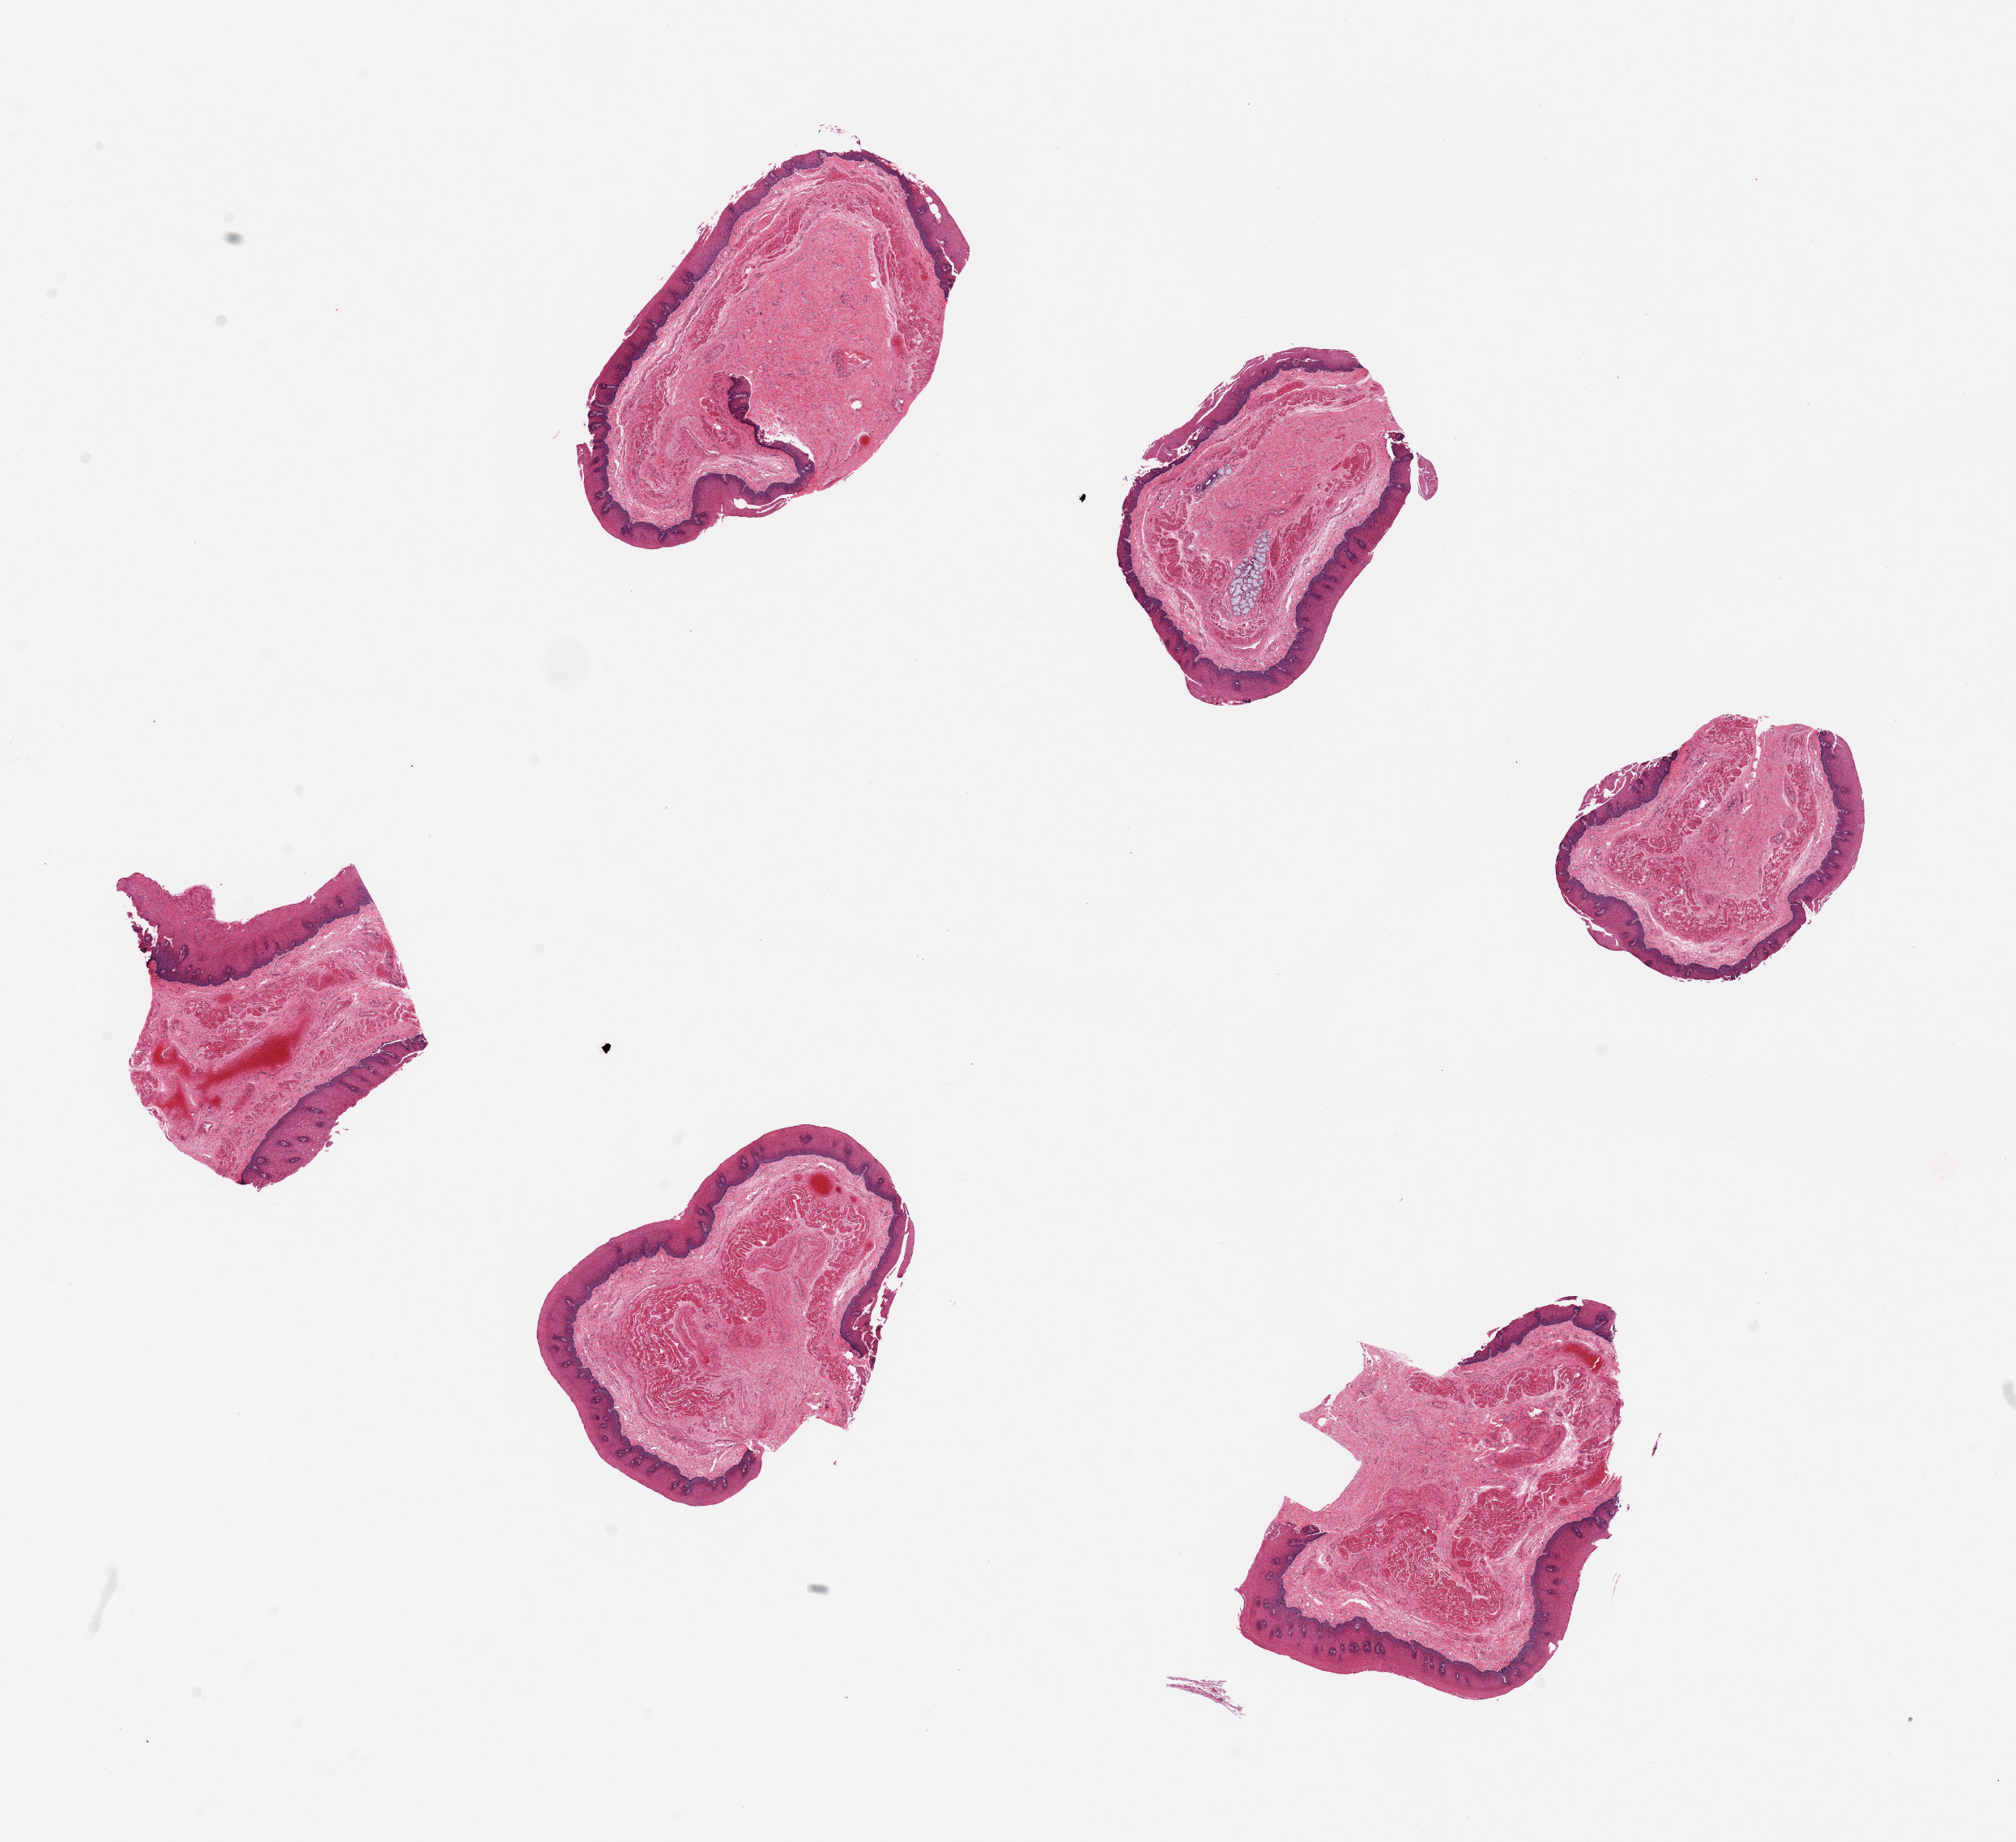
Digitized haematoxylin and eosin-stained section, brightfield — shown as a low-resolution overview of the whole scanned area (about 19.7 x 18.0 mm, from a 20x scan), PAXgene-fixed, paraffin-embedded tissue, section of esophageal mucous membrane (target tissue), donor tissue sample. Female donor.
Pathologist's review note for this sample: 6 pieces.